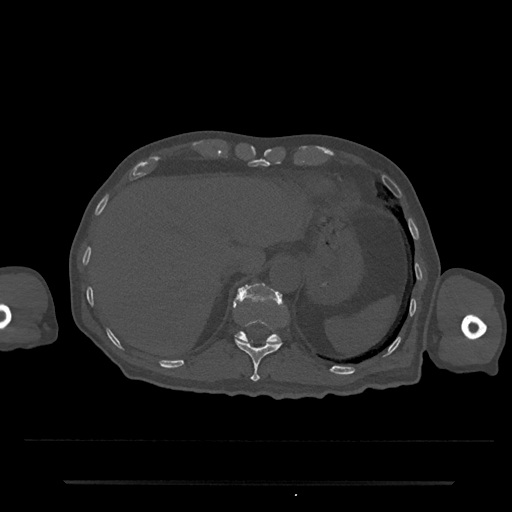
CT including the spine, one axial slice. Position 236 of 797 along the scan axis. Reconstruction kernel Br40s/3. 120 kVp. Bone window (W 1800 / L 400 HU). 0.5 mm slice thickness. 512 × 512 image matrix, field of view 427 × 427 mm. Patient: male, 74 years. From the clinical record (not read from this slice): primary cancer: prostate.
Outlined on this slice (semi-automatic segmentation, software-assisted and operator-edited):
- T11 vertebra: bounding box [x1, y1, x2, y2] px = [234, 320, 282, 382]
- T12 vertebra: [235, 283, 282, 344]